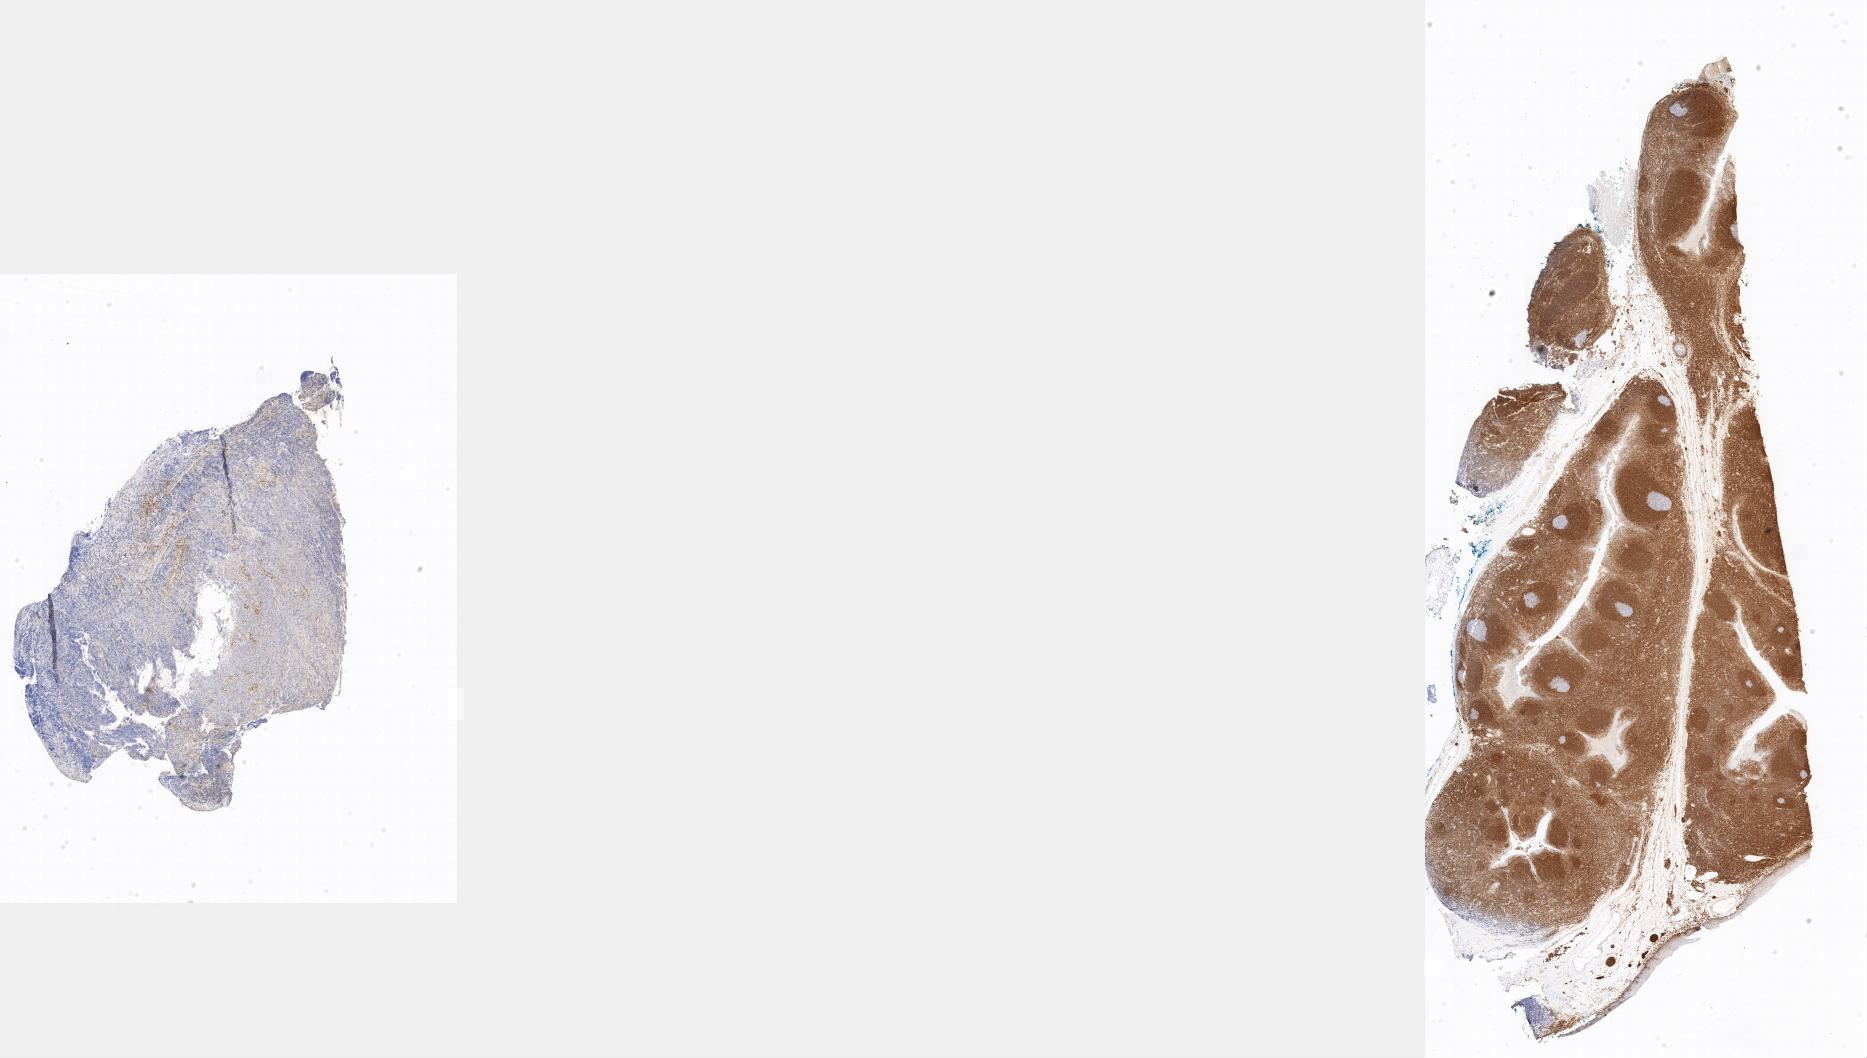
IHC for BCL2, whole-slide image, a low-resolution overview of the entire scanned area, tumor tissue, anatomic site: ovary. Patient: female, age at initial diagnosis 3 years.
Diagnosis: Burkitt lymphoma, NOS.